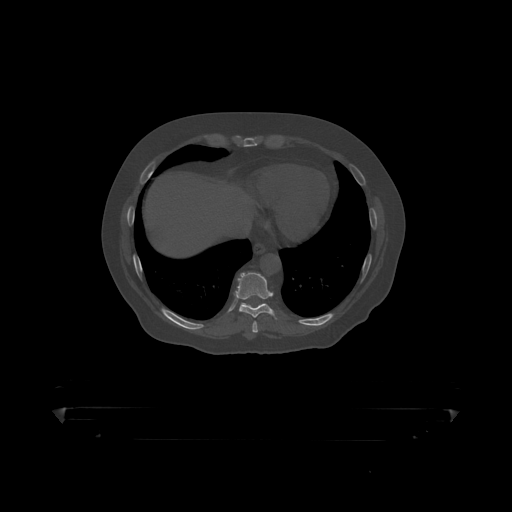
CT including the spine, one axial slice. Position 236 of 390 along the scan axis. Reconstruction kernel STANDARD. Bone window (W 1800 / L 400 HU). 1.25 mm slice thickness. 512 × 512 image matrix, field of view 650 × 650 mm. Patient: male, 60 years. From the clinical record (not read from this slice): primary cancer: prostate.
Structures marked on this image (semi-automatically segmented with operator editing):
- T9 vertebra: bounding box [x1, y1, x2, y2] px = [236, 273, 275, 318]